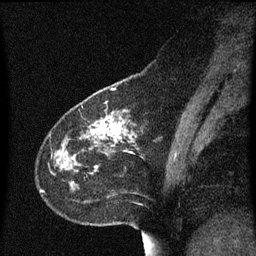
Breast MRI (dynamic contrast-enhanced), one sagittal slice; slice 20 of 60 in the series (ordered by position); dynamic contrast-enhanced series, image 2 of 3 at this slice position (ordered by acquisition); 1.5 T; TE 4.2 ms, TR 8.4 ms; 2 mm slice thickness; 256 × 256 image matrix, field of view 200 × 200 mm. Patient: female, 49 years. Case-level facts recorded for this patient, not image findings: setting: breast cancer imaged before/during neoadjuvant chemotherapy; receptor status: HR-positive, HER2-negative.
Structures marked on this image (semi-automatically segmented with operator editing):
- analysis volume of interest (the breast-tissue region the enhancement analysis was run in; not a lesion): bounding box <43,96,173,215> (left, top, right, bottom; pixels)
- tumour enhancement mask (voxels above the 70 % enhancement threshold inside the analysis volume of interest): <95,118,122,169>